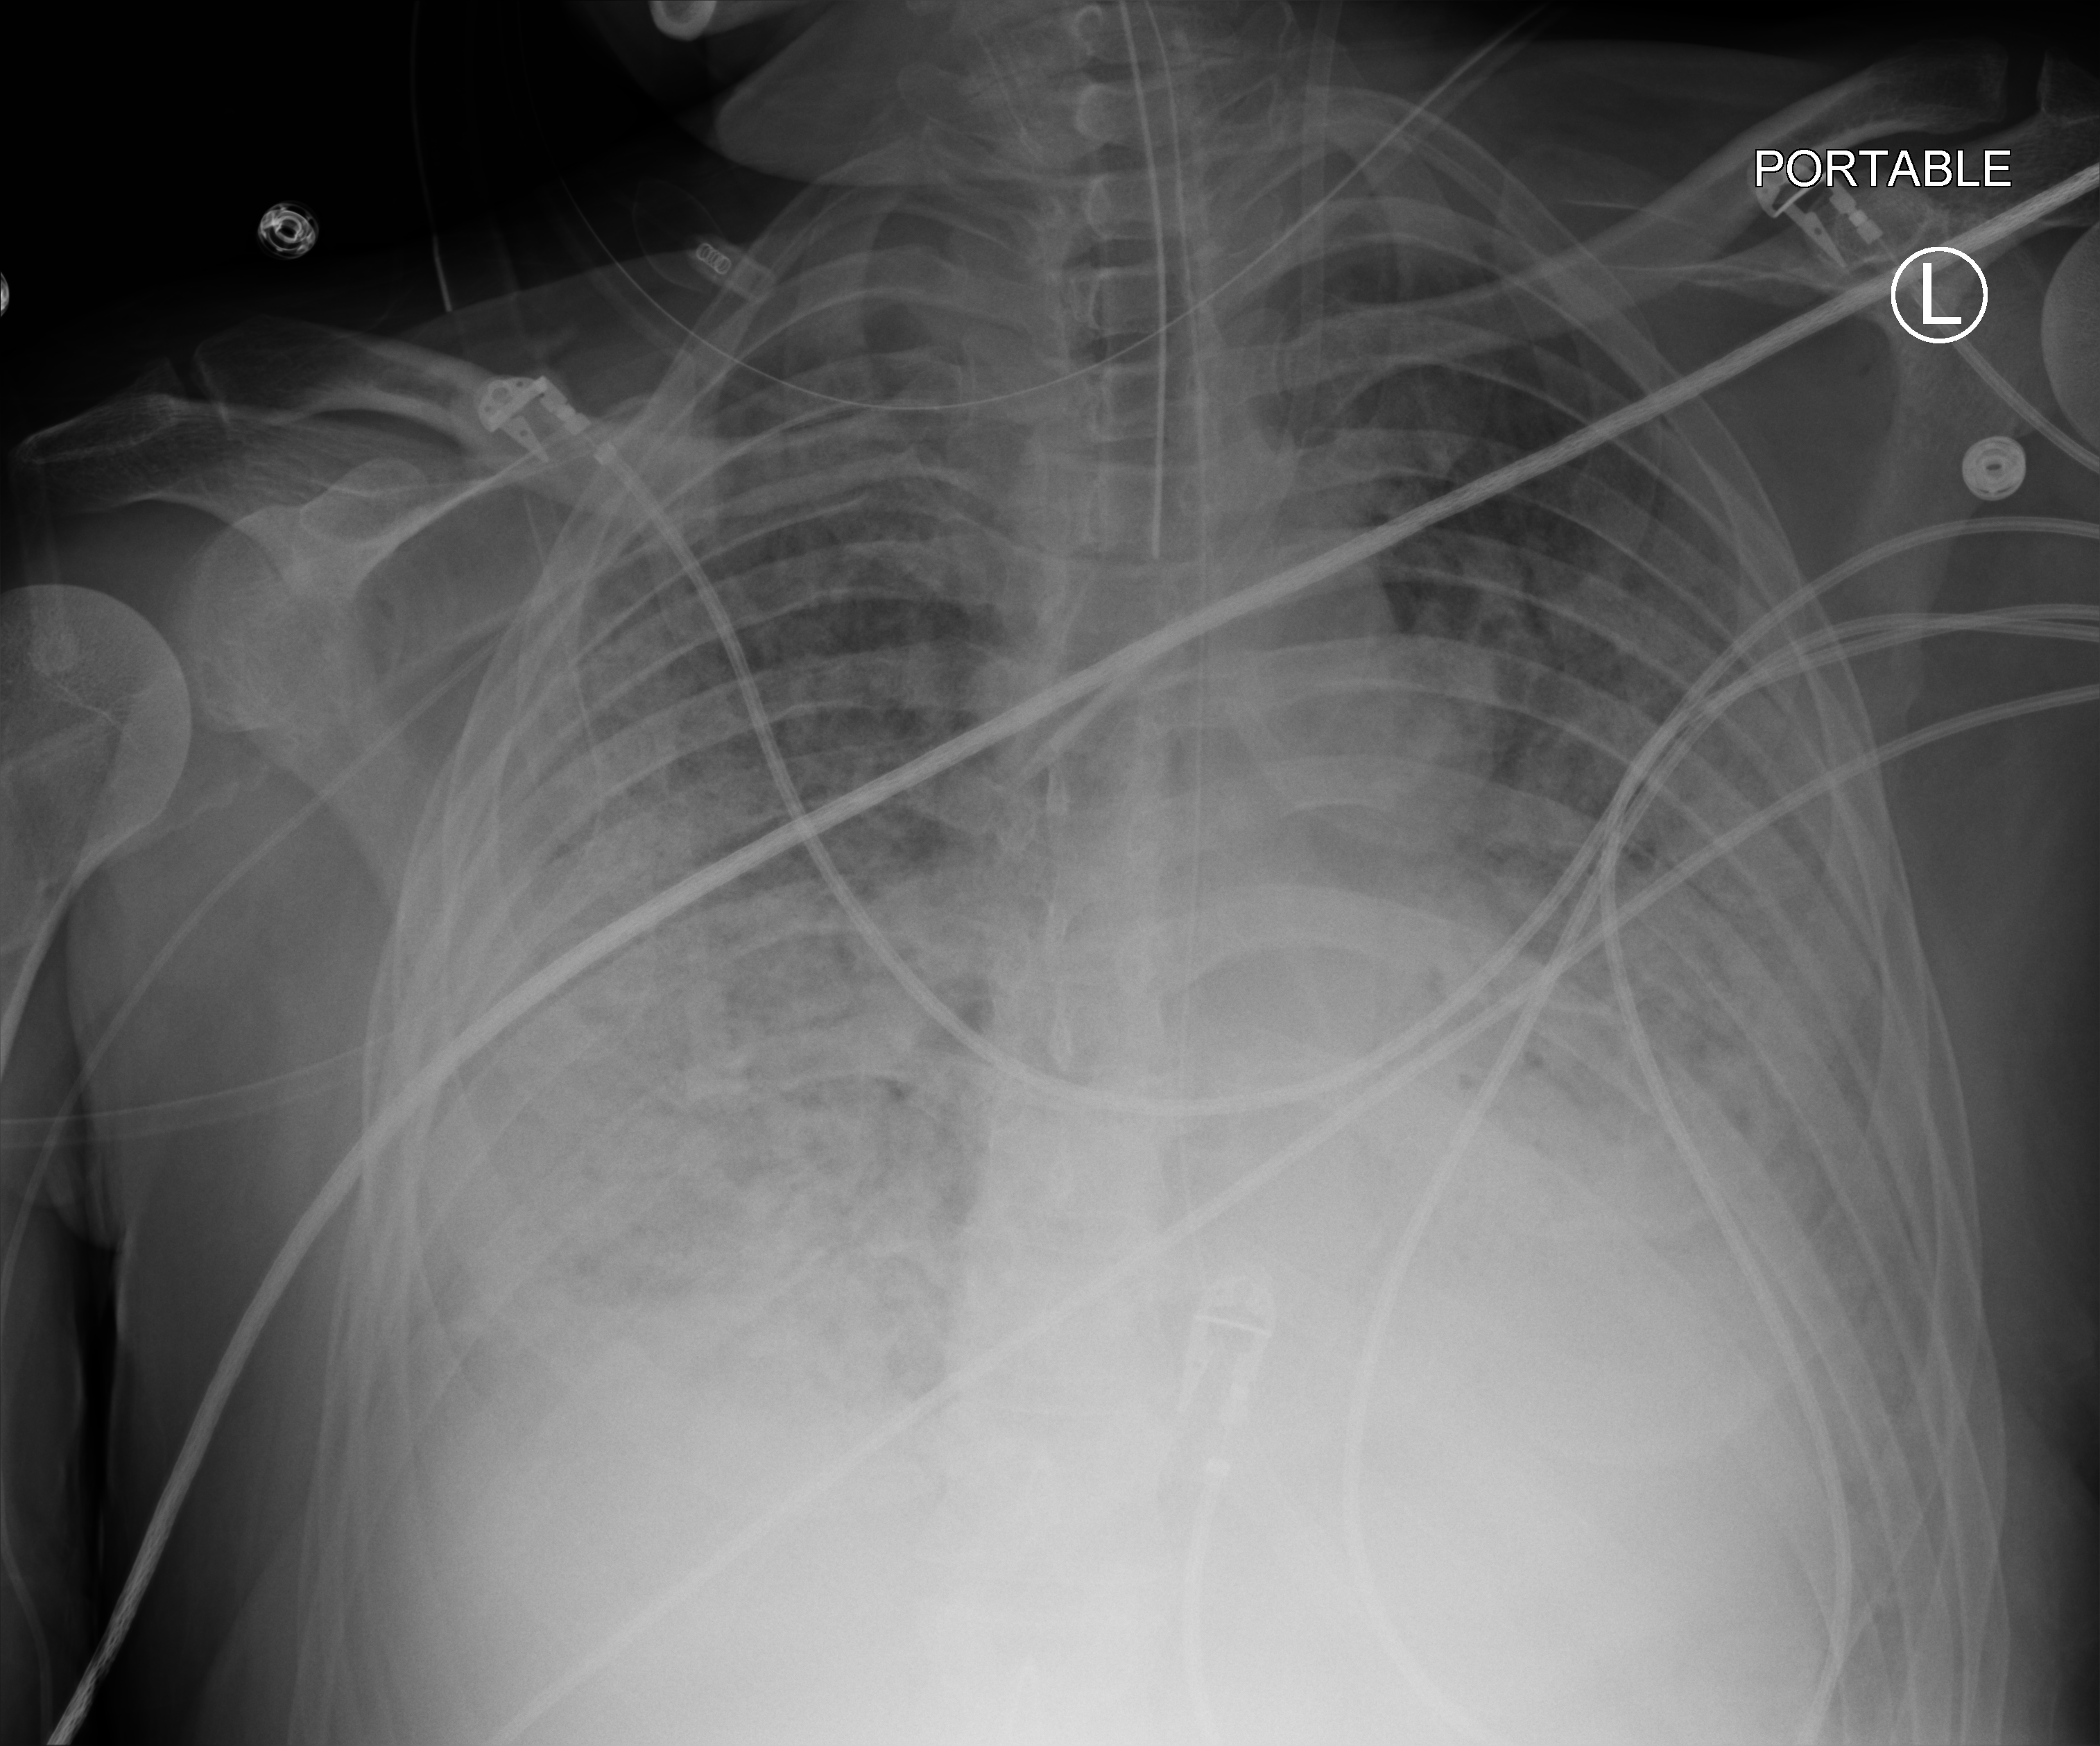
Chest X-ray (portable). Patient hospitalised with COVID-19; male, aged 18–59 years.
From the hospital-stay record, not from the radiograph (when in the stay this image was taken is not recorded): admitted to intensive care during this hospital stay: yes; mechanically ventilated during this hospital stay: yes.